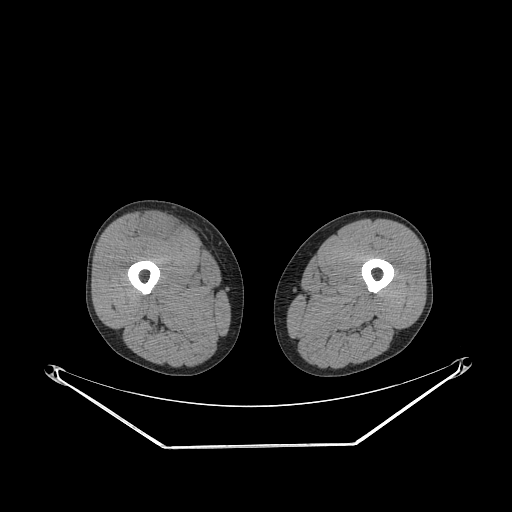
CT of an extremity soft-tissue mass (from a PET/CT study), one axial slice. 140 kVp. Soft-tissue window (W 400 / L 40 HU). 3.75 mm slice thickness. 512 × 512 image matrix, field of view 500 × 500 mm. Male patient. Case-level facts recorded for this patient, not image findings: histological type: pleiomorphic leiomyosarcoma; grade: intermediate; site of the primary tumour: right thigh.
Structures marked on this image (expert contour drawn on MRI and transferred to this co-registered scan by the dataset authors):
- gross tumour volume including surrounding oedema: bounding box (x1, y1, x2, y2) in pixels: (142, 214, 181, 241)